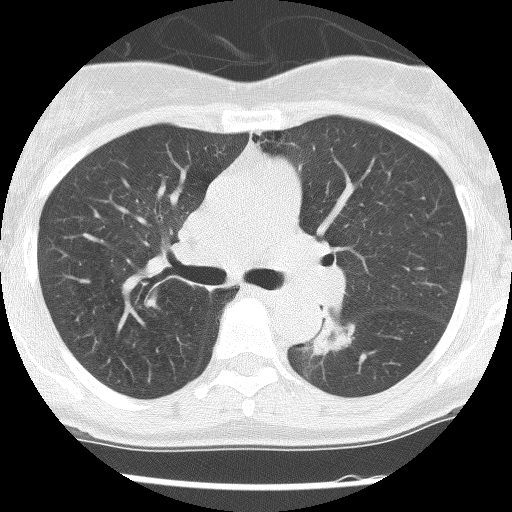
Low-dose screening chest CT, axial slice, second annual screen, lung window (W 1500 / L -600 HU), 2.5 mm slice thickness, lung (sharp) reconstruction kernel (BONE). Female participant, aged 62 years at enrolment. Former smoker at enrolment.
Lesion marked by an expert reader, bounding box (x1, y1, x2, y2) in pixels: (297, 310, 351, 356). Screening reader's record for this exam (one nodule recorded; not confirmed to be the boxed lesion): non-calcified nodule or mass ≥4 mm, right upper lobe, 30 × 30 mm, poorly defined margins, ground glass attenuation, pre-existing on the prior screen: yes; interval growth: no. Note: the box lies in the patient's left hemithorax on this image, whereas the reader's record names the right lung; they may be different findings. Official screen result: positive, no significant change: stable abnormalities potentially related to lung cancer, unchanged since the prior screening exam. Lung cancer was diagnosed 584 days after this screen: squamous cell carcinoma, NOS, left lower lobe, stage IIIB (AJCC 6th edition), 31 mm at pathology.